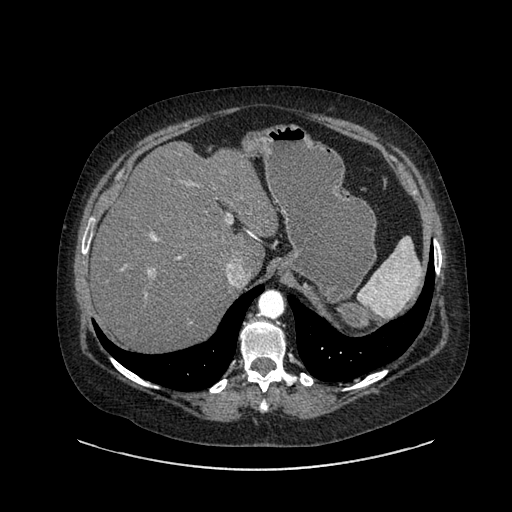
Contrast-enhanced abdominal CT, one axial slice; position 642 of 769 along the scan axis; reconstruction kernel SOFT; intravenous contrast given; soft-tissue window (W 400 / L 40 HU); 0.62 mm slice thickness; 512 × 512 image matrix, field of view 460 × 460 mm. Patient: female, 61 years. Case-level facts recorded for this patient, not image findings: diagnosis: adrenocortical carcinoma; tumour side: left adrenal; tumour size at pathology: 13 cm; Ki-67 index: 79 %; stage (as recorded): 2.
Outlined on this slice (semi-automatically segmented with operator editing):
- mass: box from (x=334, y=301) to (x=371, y=334) px